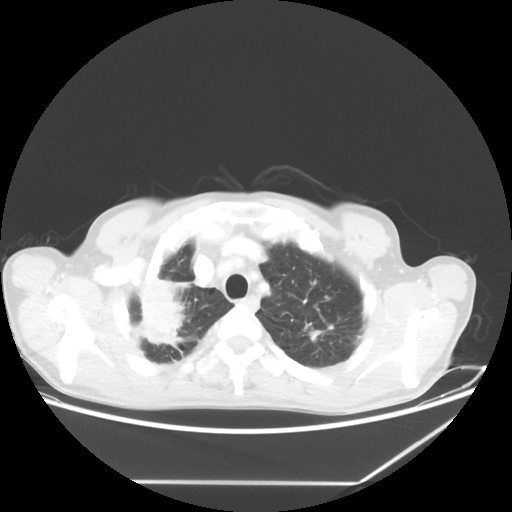
Chest CT, one axial slice; position 55 of 65 along the scan axis; reconstruction kernel STANDARD; 80 kVp; lung window (W 1500 / L -600 HU); 5 mm slice thickness; 512 × 512 image matrix, field of view 397 × 397 mm. Patient: male, 68 years. From the clinical record (not read from this slice): clinical TNM (as recorded): T3 N3 M0.
Outlined on this slice (bounding box drawn by a radiologist):
- lung tumour (recorded histology: adenocarcinoma): bounding box [x1, y1, x2, y2] px = [128, 266, 195, 365]